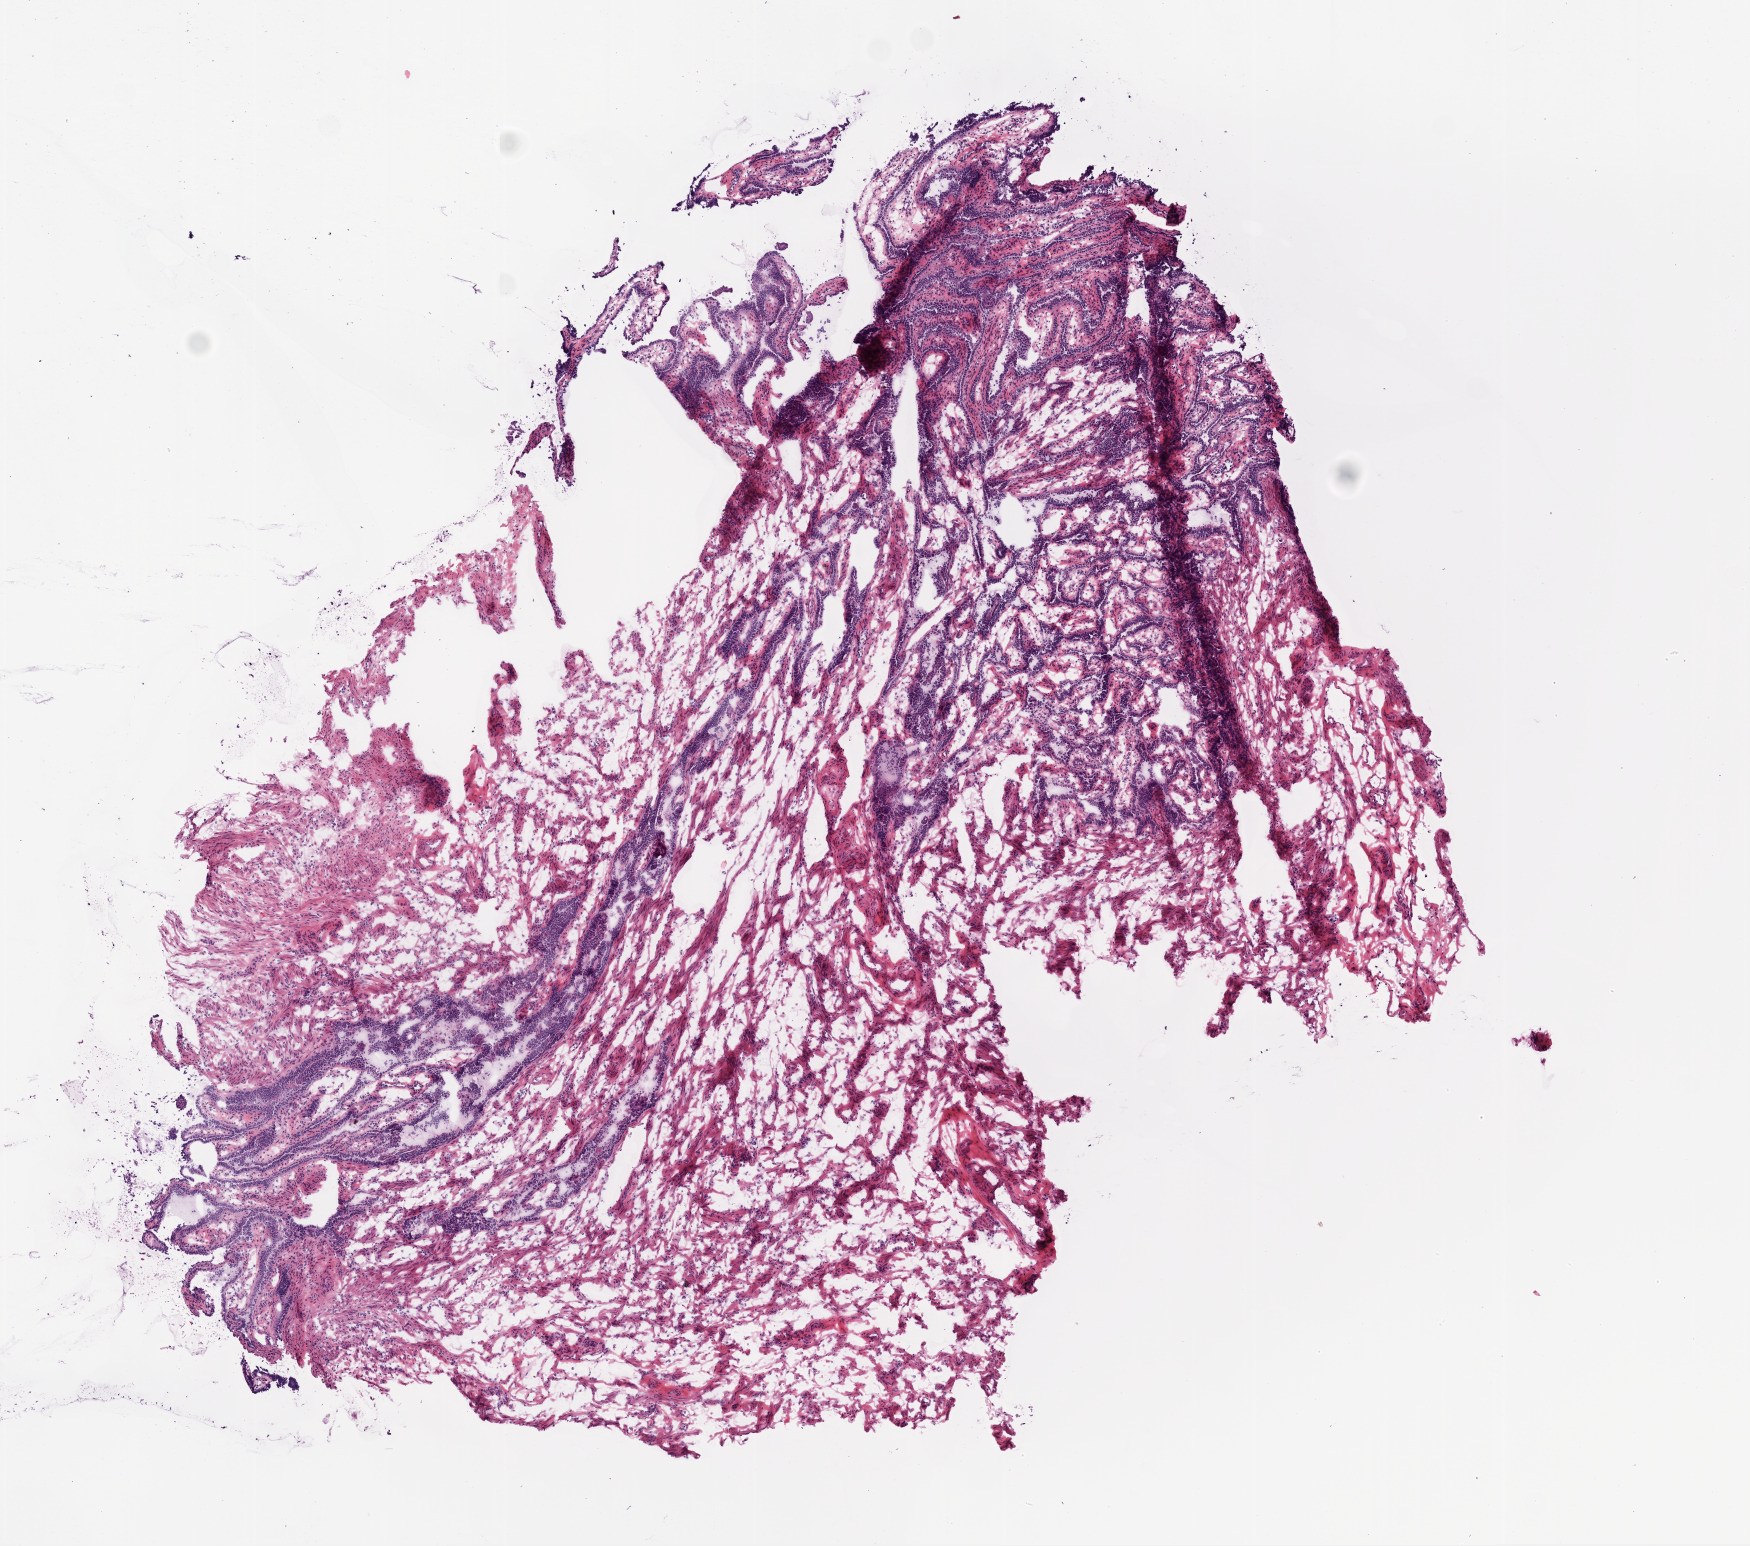
H&E whole-slide image — shown as a low-resolution overview of the whole scanned area (about 7.0 x 6.2 mm, from a 20x scan). Frozen section. Sample: solid tissue normal (non-tumour tissue), ovary. Female patient; age at initial diagnosis 54 years.
This section: solid tissue normal (non-tumour) sample from the same patient. Patient diagnosis: Serous cystadenocarcinoma, NOS.